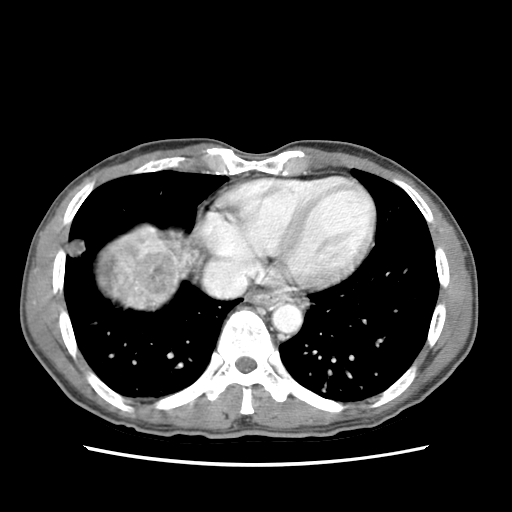
Contrast-enhanced abdominal CT (liver protocol), one axial slice. Position 71 of 79 along the scan axis. Soft-tissue window (W 400 / L 40 HU). 2.5 mm slice thickness. 512 × 512 image matrix, field of view 320 × 320 mm. From the clinical record (not read from this slice): diagnosis: hepatocellular carcinoma (patient treated with transarterial chemoembolisation; whether this scan precedes or follows treatment is not stated here); TNM stage (as recorded): Stage-IIIB; Child-Pugh class: A; tumour differentiation: moderately differentiated; tumour nodularity: multinodular.
Structures marked on this image (semi-automatic segmentation, software-assisted and operator-edited):
- liver parenchyma outside the tumour (the mass and vessels are separate outlines, so this box may not span the whole liver): bounding box (x1, y1, x2, y2) in pixels: (94, 221, 196, 308)
- mass: (99, 226, 183, 310)
- liver vessels: (145, 222, 192, 279)